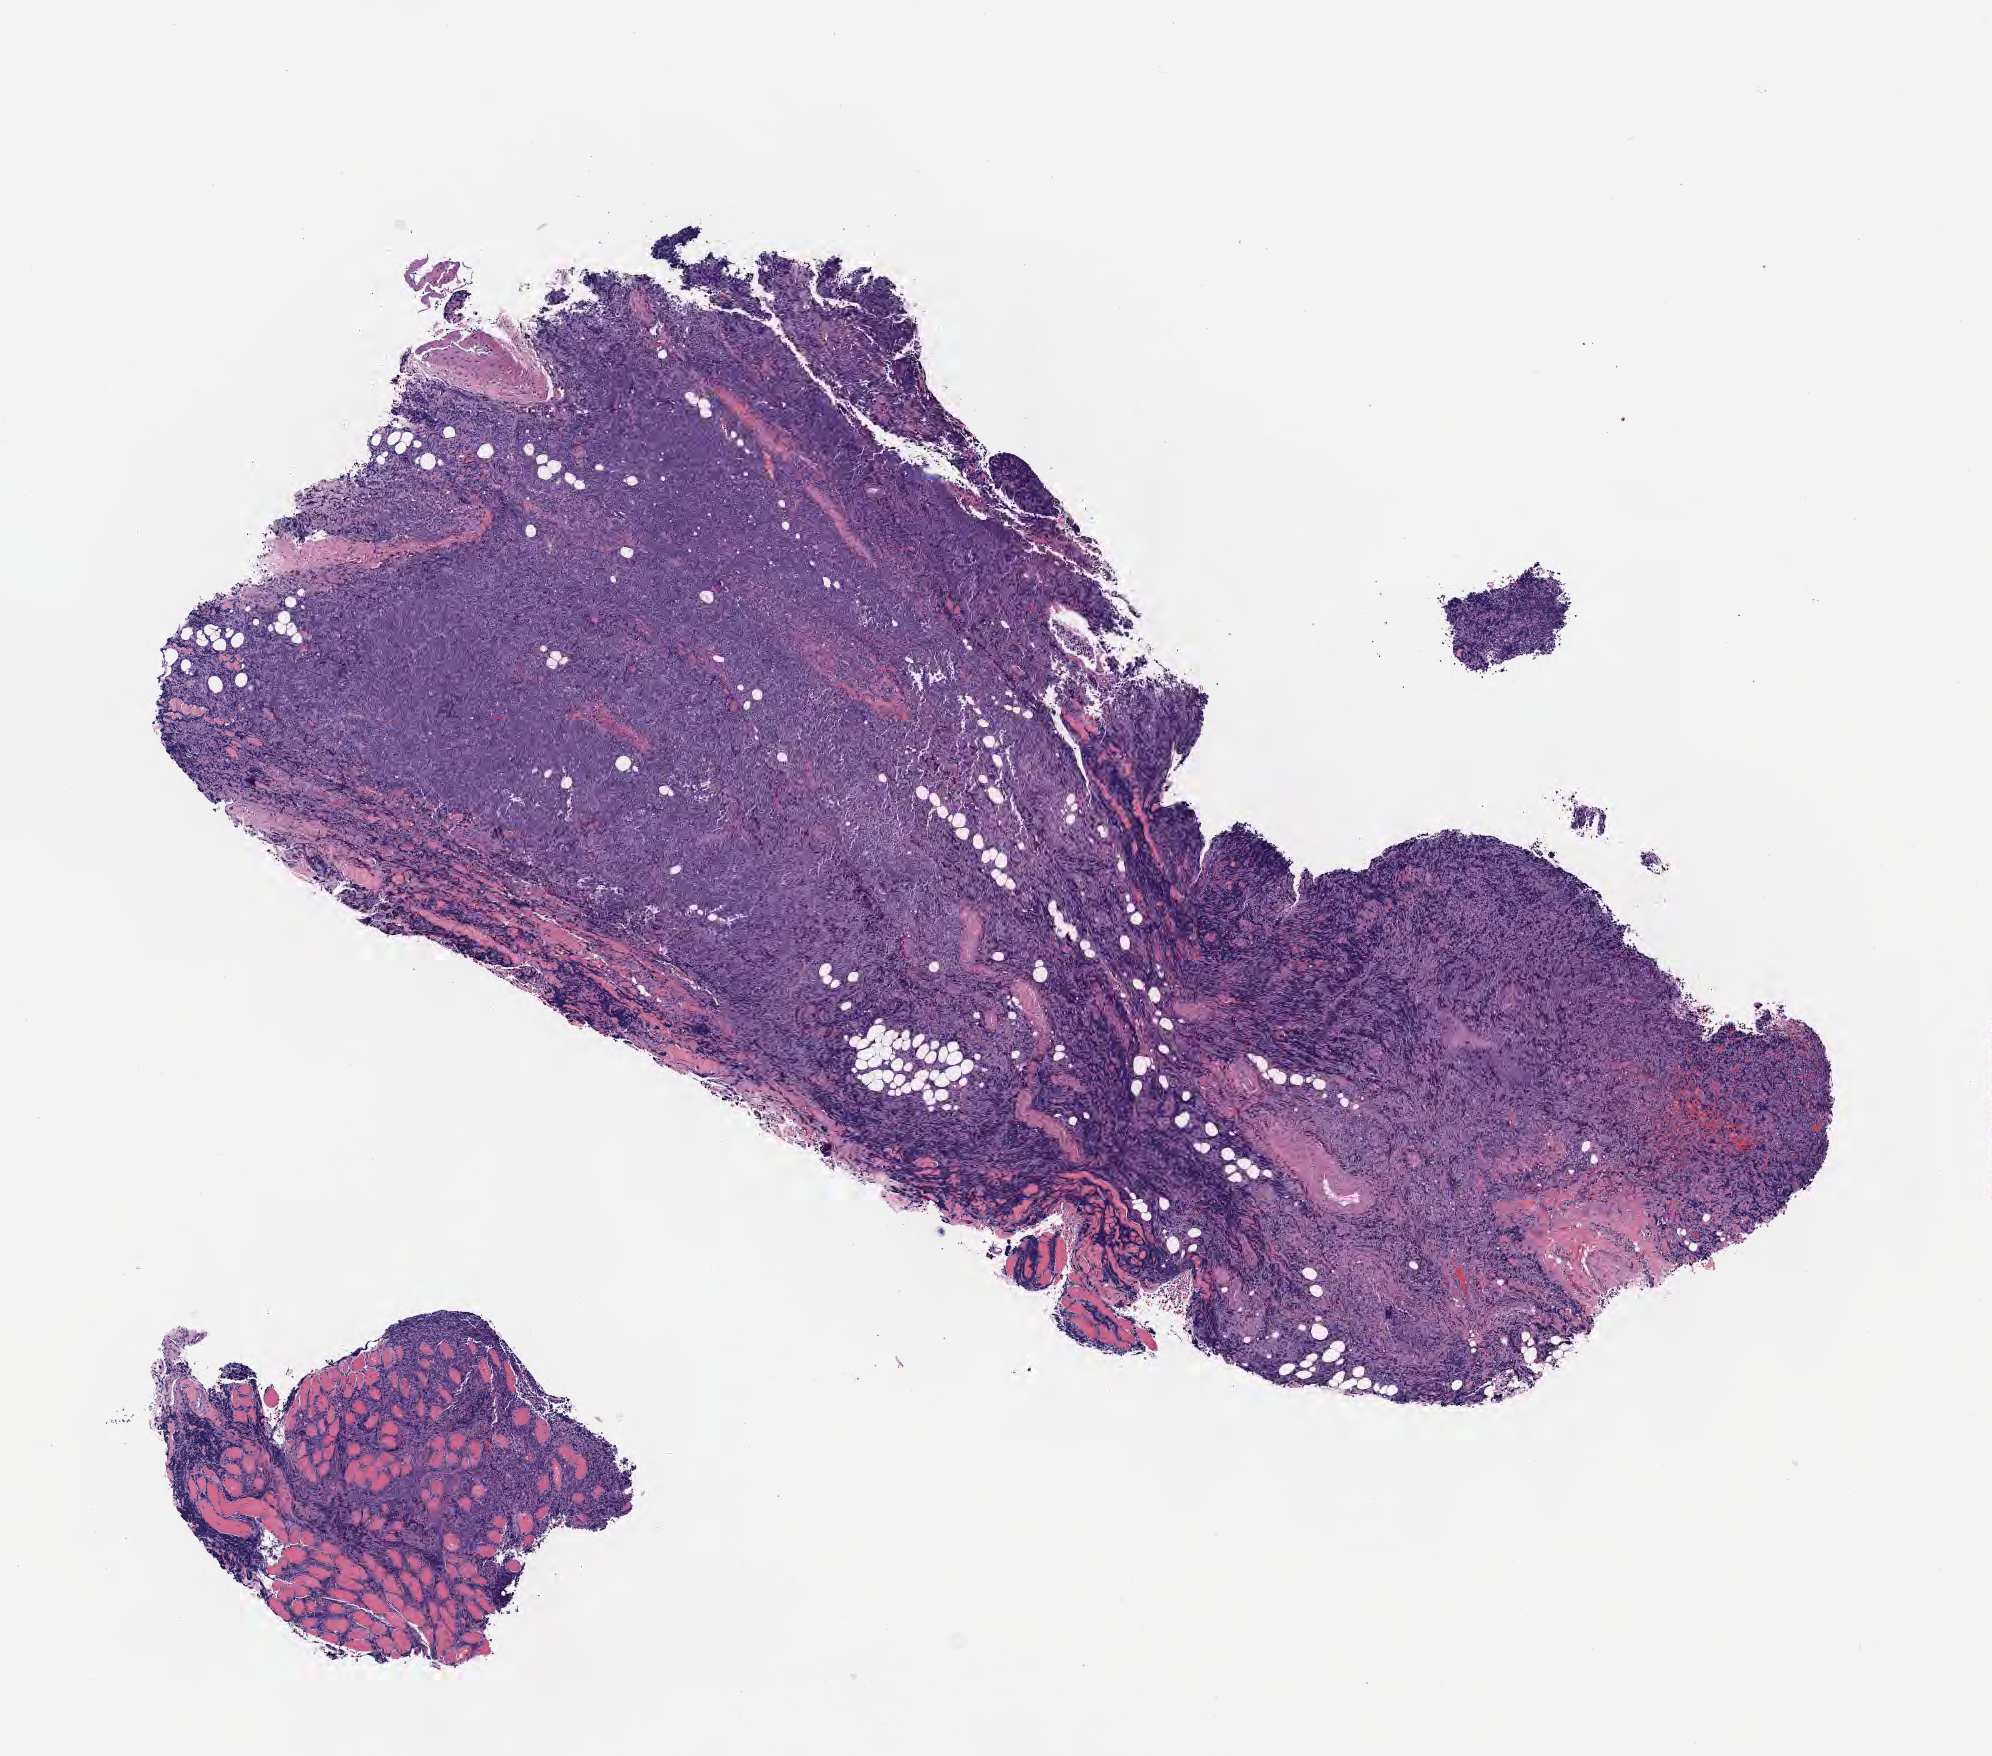
Digitized H&E-stained section, a low-resolution overview of the entire scanned area, about 8.0 x 7.1 mm; tumor tissue. Male patient, aged 67.
Histologic diagnosis: Diffuse large B-cell lymphoma, NOS.